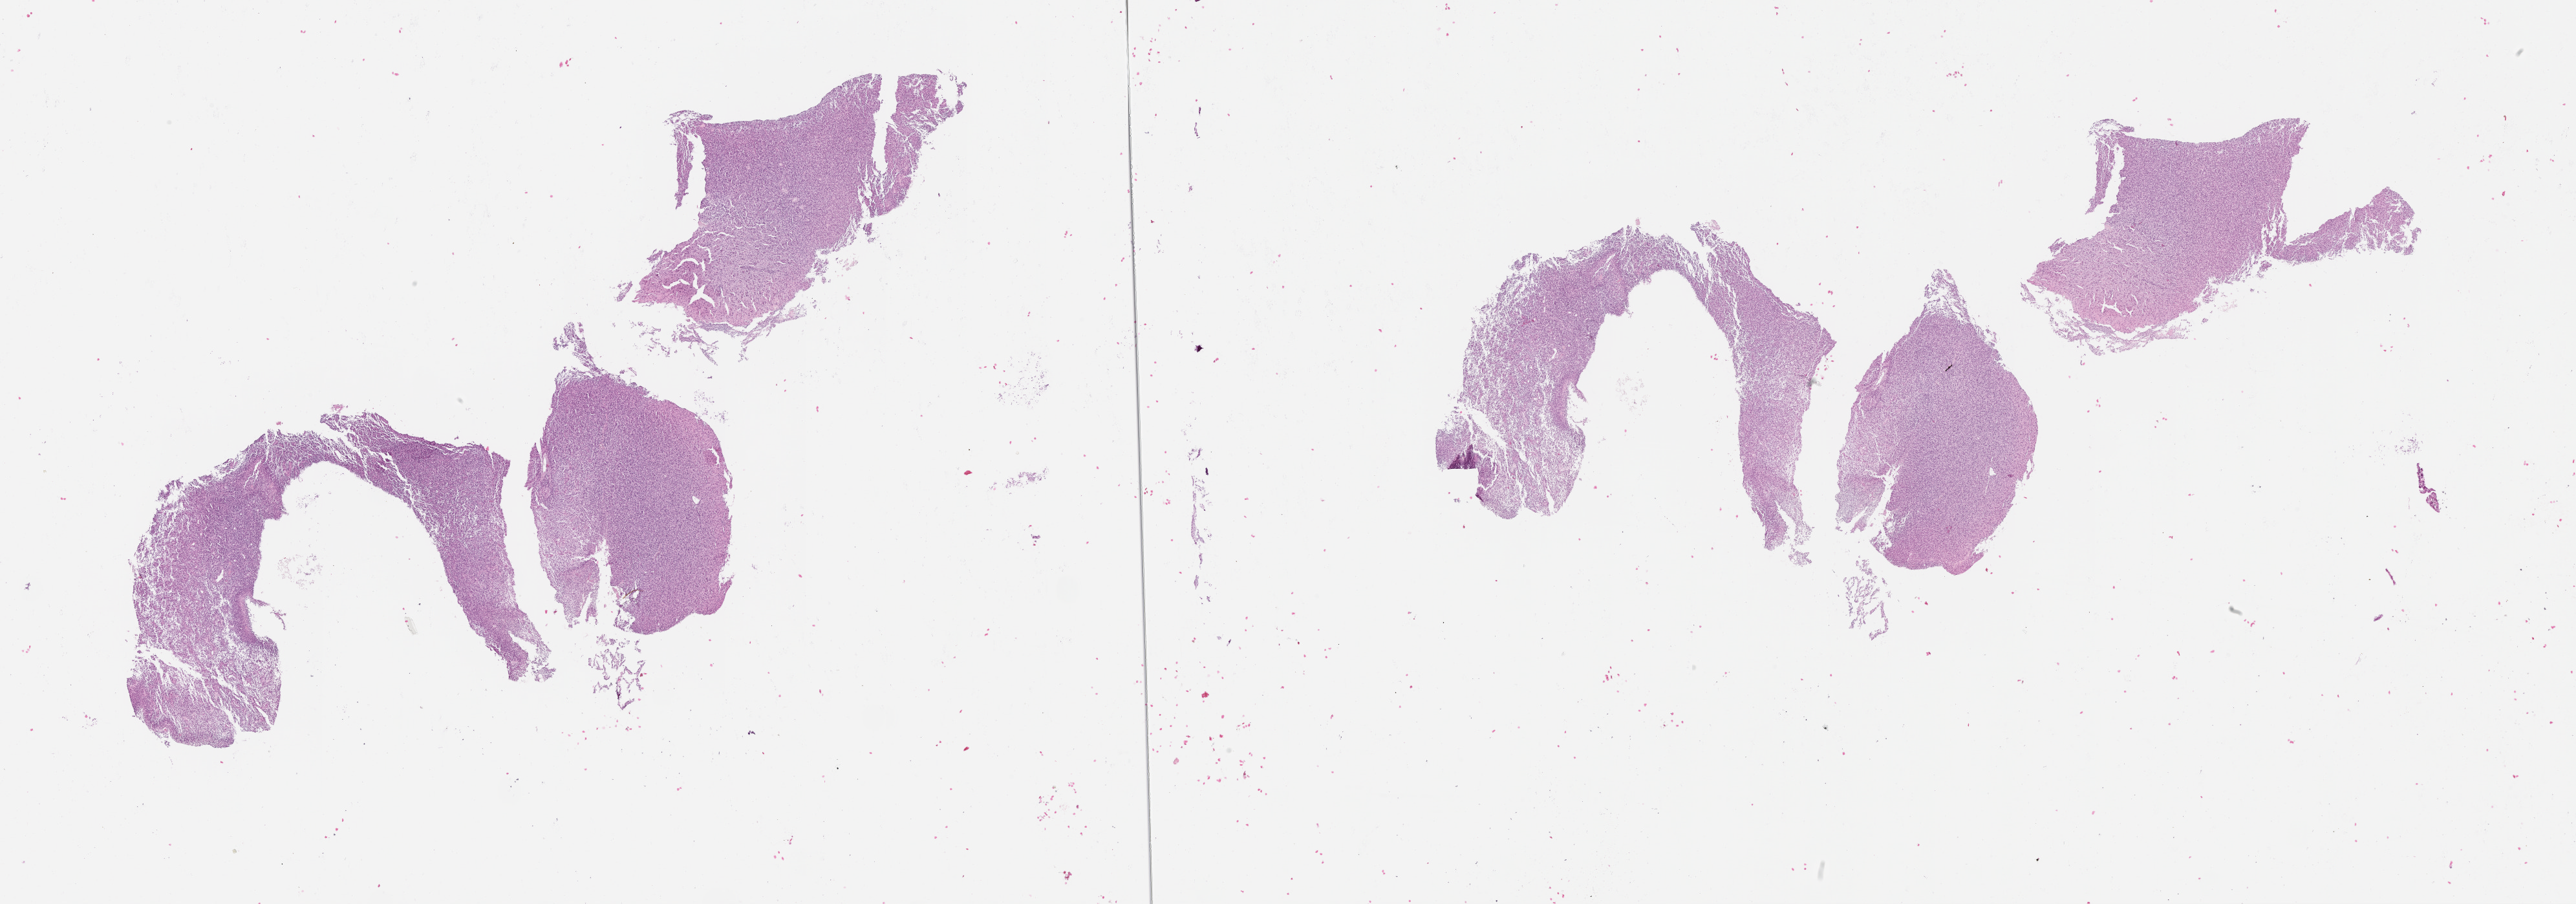
Hematoxylin and eosin (H&E) stained whole-slide image — low-resolution overview of the scanned area, about 32.1 x 11.3 mm; tumour tissue sample, sampled site: frontal lobe. Female, 80 y/o. Slide review estimates, as recorded: tumour nuclei 90%, necrosis 5%.
Histologic diagnosis: Glioblastoma.